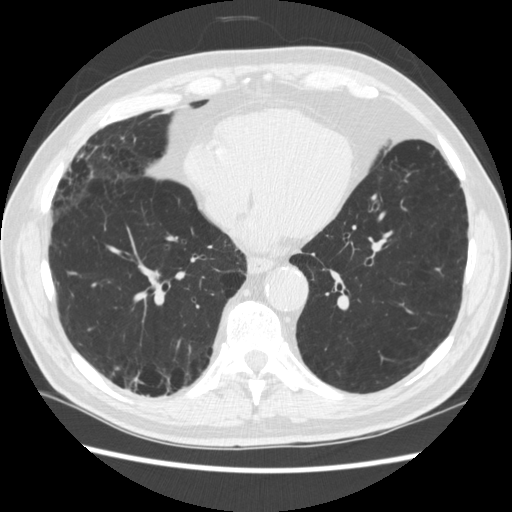
Low-dose screening chest CT, axial slice. Third screening round (two years after baseline). Lung window (W 1500 / L -600 HU). Standard (soft-tissue) reconstruction kernel (STANDARD). Slice 167 of 266 in the series. Male, age 70 years at enrolment. Former smoker at enrolment.
Expert reader's lesion annotation, bounding box <132,358,175,411> (left, top, right, bottom; pixels). The screening reader recorded 4 non-calcified nodules or masses ≥4 mm on this exam (right lower lobe, right lower lobe, left lower lobe, left lower lobe); which of them this box marks is not recorded. Later outcome: lung cancer diagnosed 253 days after this screen — squamous cell carcinoma, NOS, right upper lobe, poorly differentiated (G3), stage IV (AJCC 6th edition).